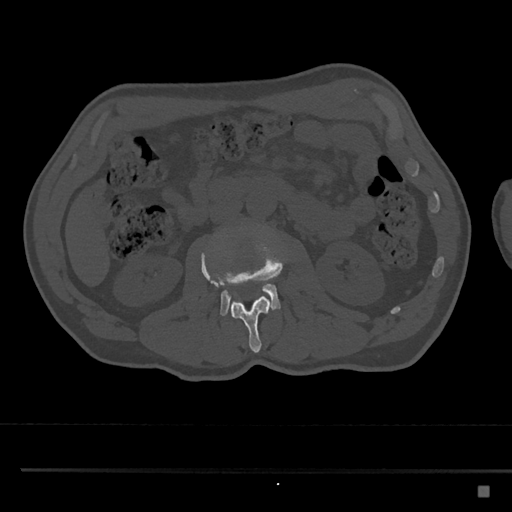
CT including the spine, one axial slice; position 735 of 797 along the scan axis; 120 kVp; bone window (W 1800 / L 400 HU); 0.5 mm slice thickness; 512 × 512 image matrix, field of view 391 × 391 mm. Patient: male, 59 years. From the clinical record (not read from this slice): primary cancer: prostate.
Outlined on this slice (semi-automatic segmentation, software-assisted and operator-edited):
- L2 vertebra: box from (x=201, y=235) to (x=282, y=353) px
- L3 vertebra: (x=201, y=230)–(x=281, y=317)